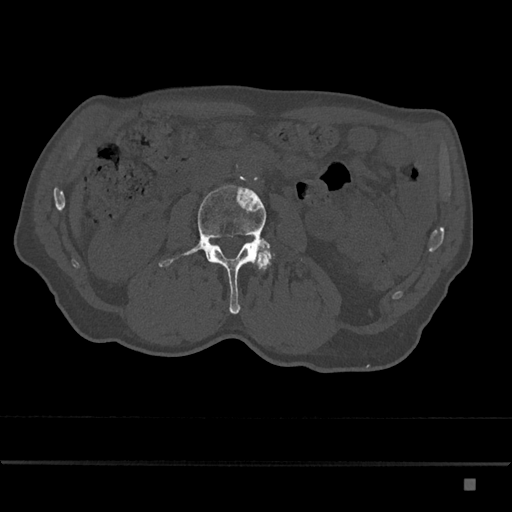
CT including the spine, one axial slice; position 404 of 797 along the scan axis; reconstruction kernel Br40s/3; 120 kVp; bone window (W 1800 / L 400 HU); 0.5 mm slice thickness; 512 × 512 image matrix, field of view 390 × 390 mm. Patient: male, 72 years. Case-level facts recorded for this patient, not image findings: primary cancer: prostate.
Annotated regions visible in this slice (semi-automatically segmented with operator editing):
- L3 vertebra: bounding box <158,185,271,314> (left, top, right, bottom; pixels)
- L4 vertebra: <256,250,273,271>